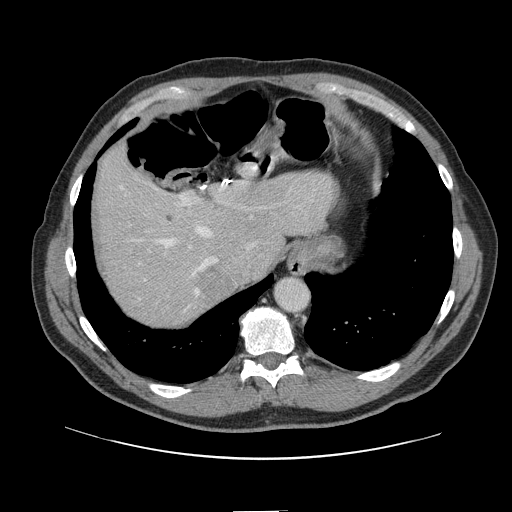
Contrast-enhanced abdominal CT, one axial slice. Position 114 of 161 along the scan axis. 120 kVp. Intravenous contrast given. Soft-tissue window (W 400 / L 40 HU). 512 × 512 image matrix. Male patient, age 66 years. From the clinical record (not read from this slice): diagnosis: colorectal cancer liver metastases, imaged before liver resection; multiple liver metastases: no; largest metastasis: 3.5 cm; disease in both lobes: no.
Outlined on this slice (outlined manually by an expert reader):
- hepatic veins: bounding box <120,186,253,300> (left, top, right, bottom; pixels)
- liver: <97,149,326,326>
- planned liver remnant (the part of the liver to remain after resection): <97,151,327,304>
- portal vein (with intrahepatic branches): <180,189,273,248>
- liver metastasis: <191,267,227,301>